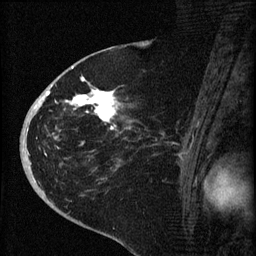
Breast MRI (dynamic contrast-enhanced), one sagittal slice. Dynamic contrast-enhanced series, image 2 of 4 at this slice position (ordered by acquisition). 1.5 T. TE 4.2 ms, TR 8.2 ms. 256 × 256 image matrix. Female patient, age 71 years.
Structures marked on this image (semi-automatically segmented with operator editing):
- analysis volume of interest (the breast-tissue region the enhancement analysis was run in; not a lesion): bounding box (x1, y1, x2, y2) in pixels: (35, 75, 152, 190)
- tumour enhancement mask (voxels above the 70 % enhancement threshold inside the analysis volume of interest): (36, 77, 119, 144)